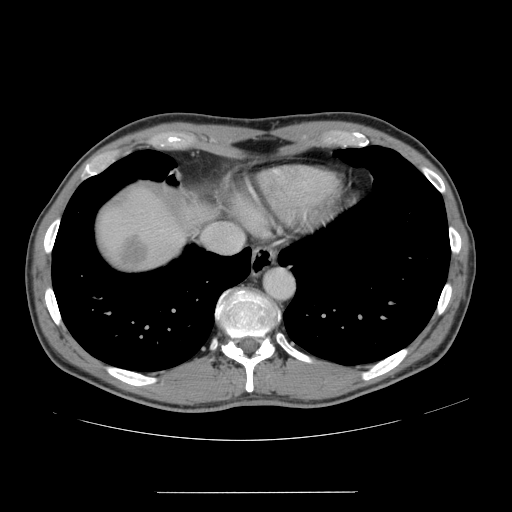
Contrast-enhanced abdominal CT, one axial slice. Slice 140 of 178 in the series (ordered by position). 120 kVp. Intravenous contrast given. Soft-tissue window (W 400 / L 40 HU). 2.5 mm slice thickness. 512 × 512 image matrix, field of view 401 × 401 mm. Male patient, age 53 years. From the clinical record (not read from this slice): diagnosis: colorectal cancer liver metastases, imaged before liver resection; multiple liver metastases: yes; largest metastasis: 2.4 cm.
Annotated regions visible in this slice (manually delineated by an expert):
- liver: bounding box (x1, y1, x2, y2) in pixels: (97, 186, 187, 270)
- liver metastasis: (119, 235, 150, 267)